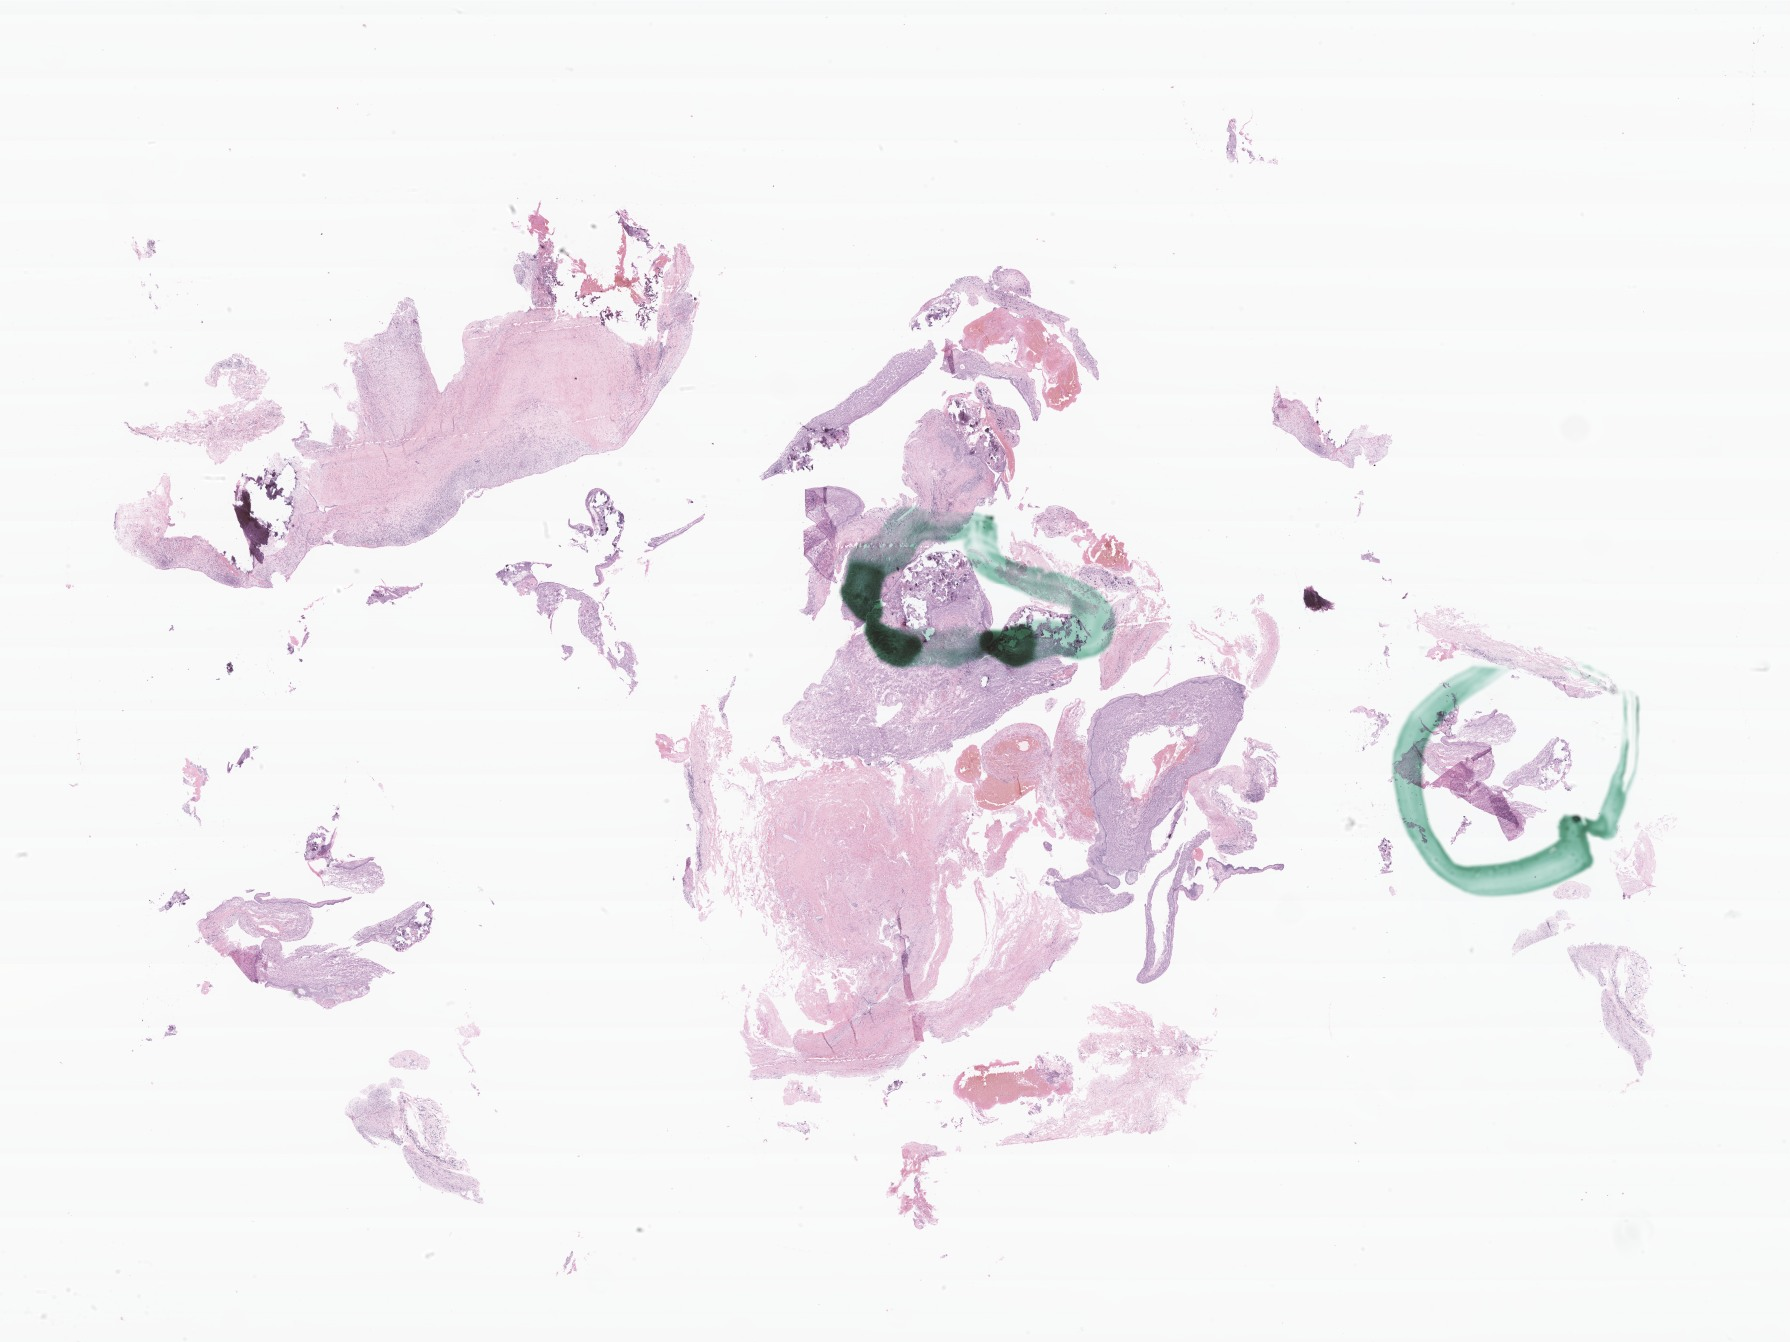
Whole-slide image, haematoxylin and eosin stain of tumor tissue from the brain, low-resolution overview of the scanned area, about 30.1 x 22.6 mm; formalin-fixed paraffin-embedded section. Patient: male, age 173 months (14 years 5 months).
Recorded diagnosis: Craniopharyngioma, NOS.